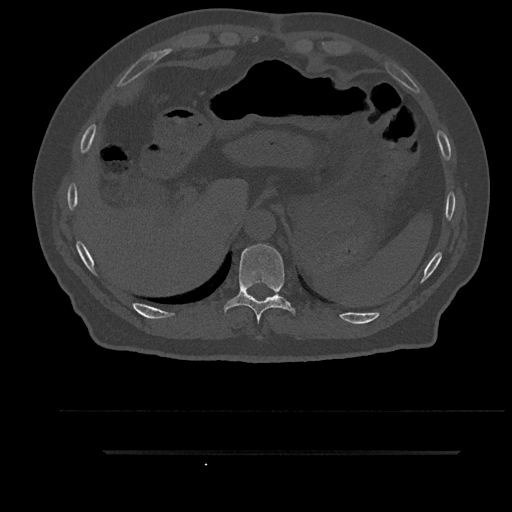
CT including the spine, one axial slice; position 362 of 797 along the scan axis; reconstruction kernel Br40s/3; 120 kVp; bone window (W 1800 / L 400 HU); 512 × 512 image matrix, field of view 432 × 432 mm. Male patient, age 63 years. From the clinical record (not read from this slice): primary cancer: renal; vertebrae with lytic lesions (as recorded): T8.
Outlined on this slice (semi-automatically segmented with operator editing):
- T10 vertebra: bounding box <223,244,296,323> (left, top, right, bottom; pixels)